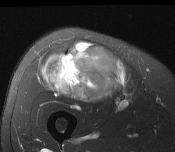
MRI of an extremity soft-tissue mass, one axial slice. T2-weighted fat-saturated. MR volume resampled by the dataset authors to the PET/CT grid (not the native acquisition matrix). 3.27 mm slice thickness. 175 × 152 image matrix, field of view 171 × 148 mm. Male patient. From the clinical record (not read from this slice): histological type: pleiomorphic leiomyosarcoma; grade: intermediate; site of the primary tumour: right thigh.
Outlined on this slice (expert contour drawn on MRI and transferred to this co-registered scan by the dataset authors):
- gross tumour volume including surrounding oedema: bounding box <42,42,125,103> (left, top, right, bottom; pixels)
- gross tumour volume (mass): <42,42,125,103>